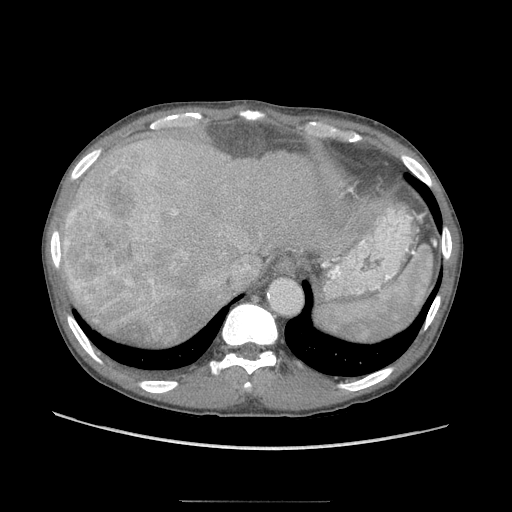
Contrast-enhanced abdominal CT (liver protocol), one axial slice. Position 78 of 103 along the scan axis. Reconstruction kernel STANDARD. Soft-tissue window (W 400 / L 40 HU). 2.5 mm slice thickness. 512 × 512 image matrix, field of view 380 × 380 mm. From the clinical record (not read from this slice): diagnosis: hepatocellular carcinoma (patient treated with transarterial chemoembolisation; whether this scan precedes or follows treatment is not stated here); TNM stage (as recorded): Stage-IIIA; Child-Pugh class: A.
Structures marked on this image (semi-automatic segmentation, software-assisted and operator-edited):
- liver parenchyma outside the tumour (the mass and vessels are separate outlines, so this box may not span the whole liver): bounding box (x1, y1, x2, y2) in pixels: (62, 123, 324, 340)
- mass: (65, 173, 189, 337)
- liver vessels: (120, 259, 269, 292)